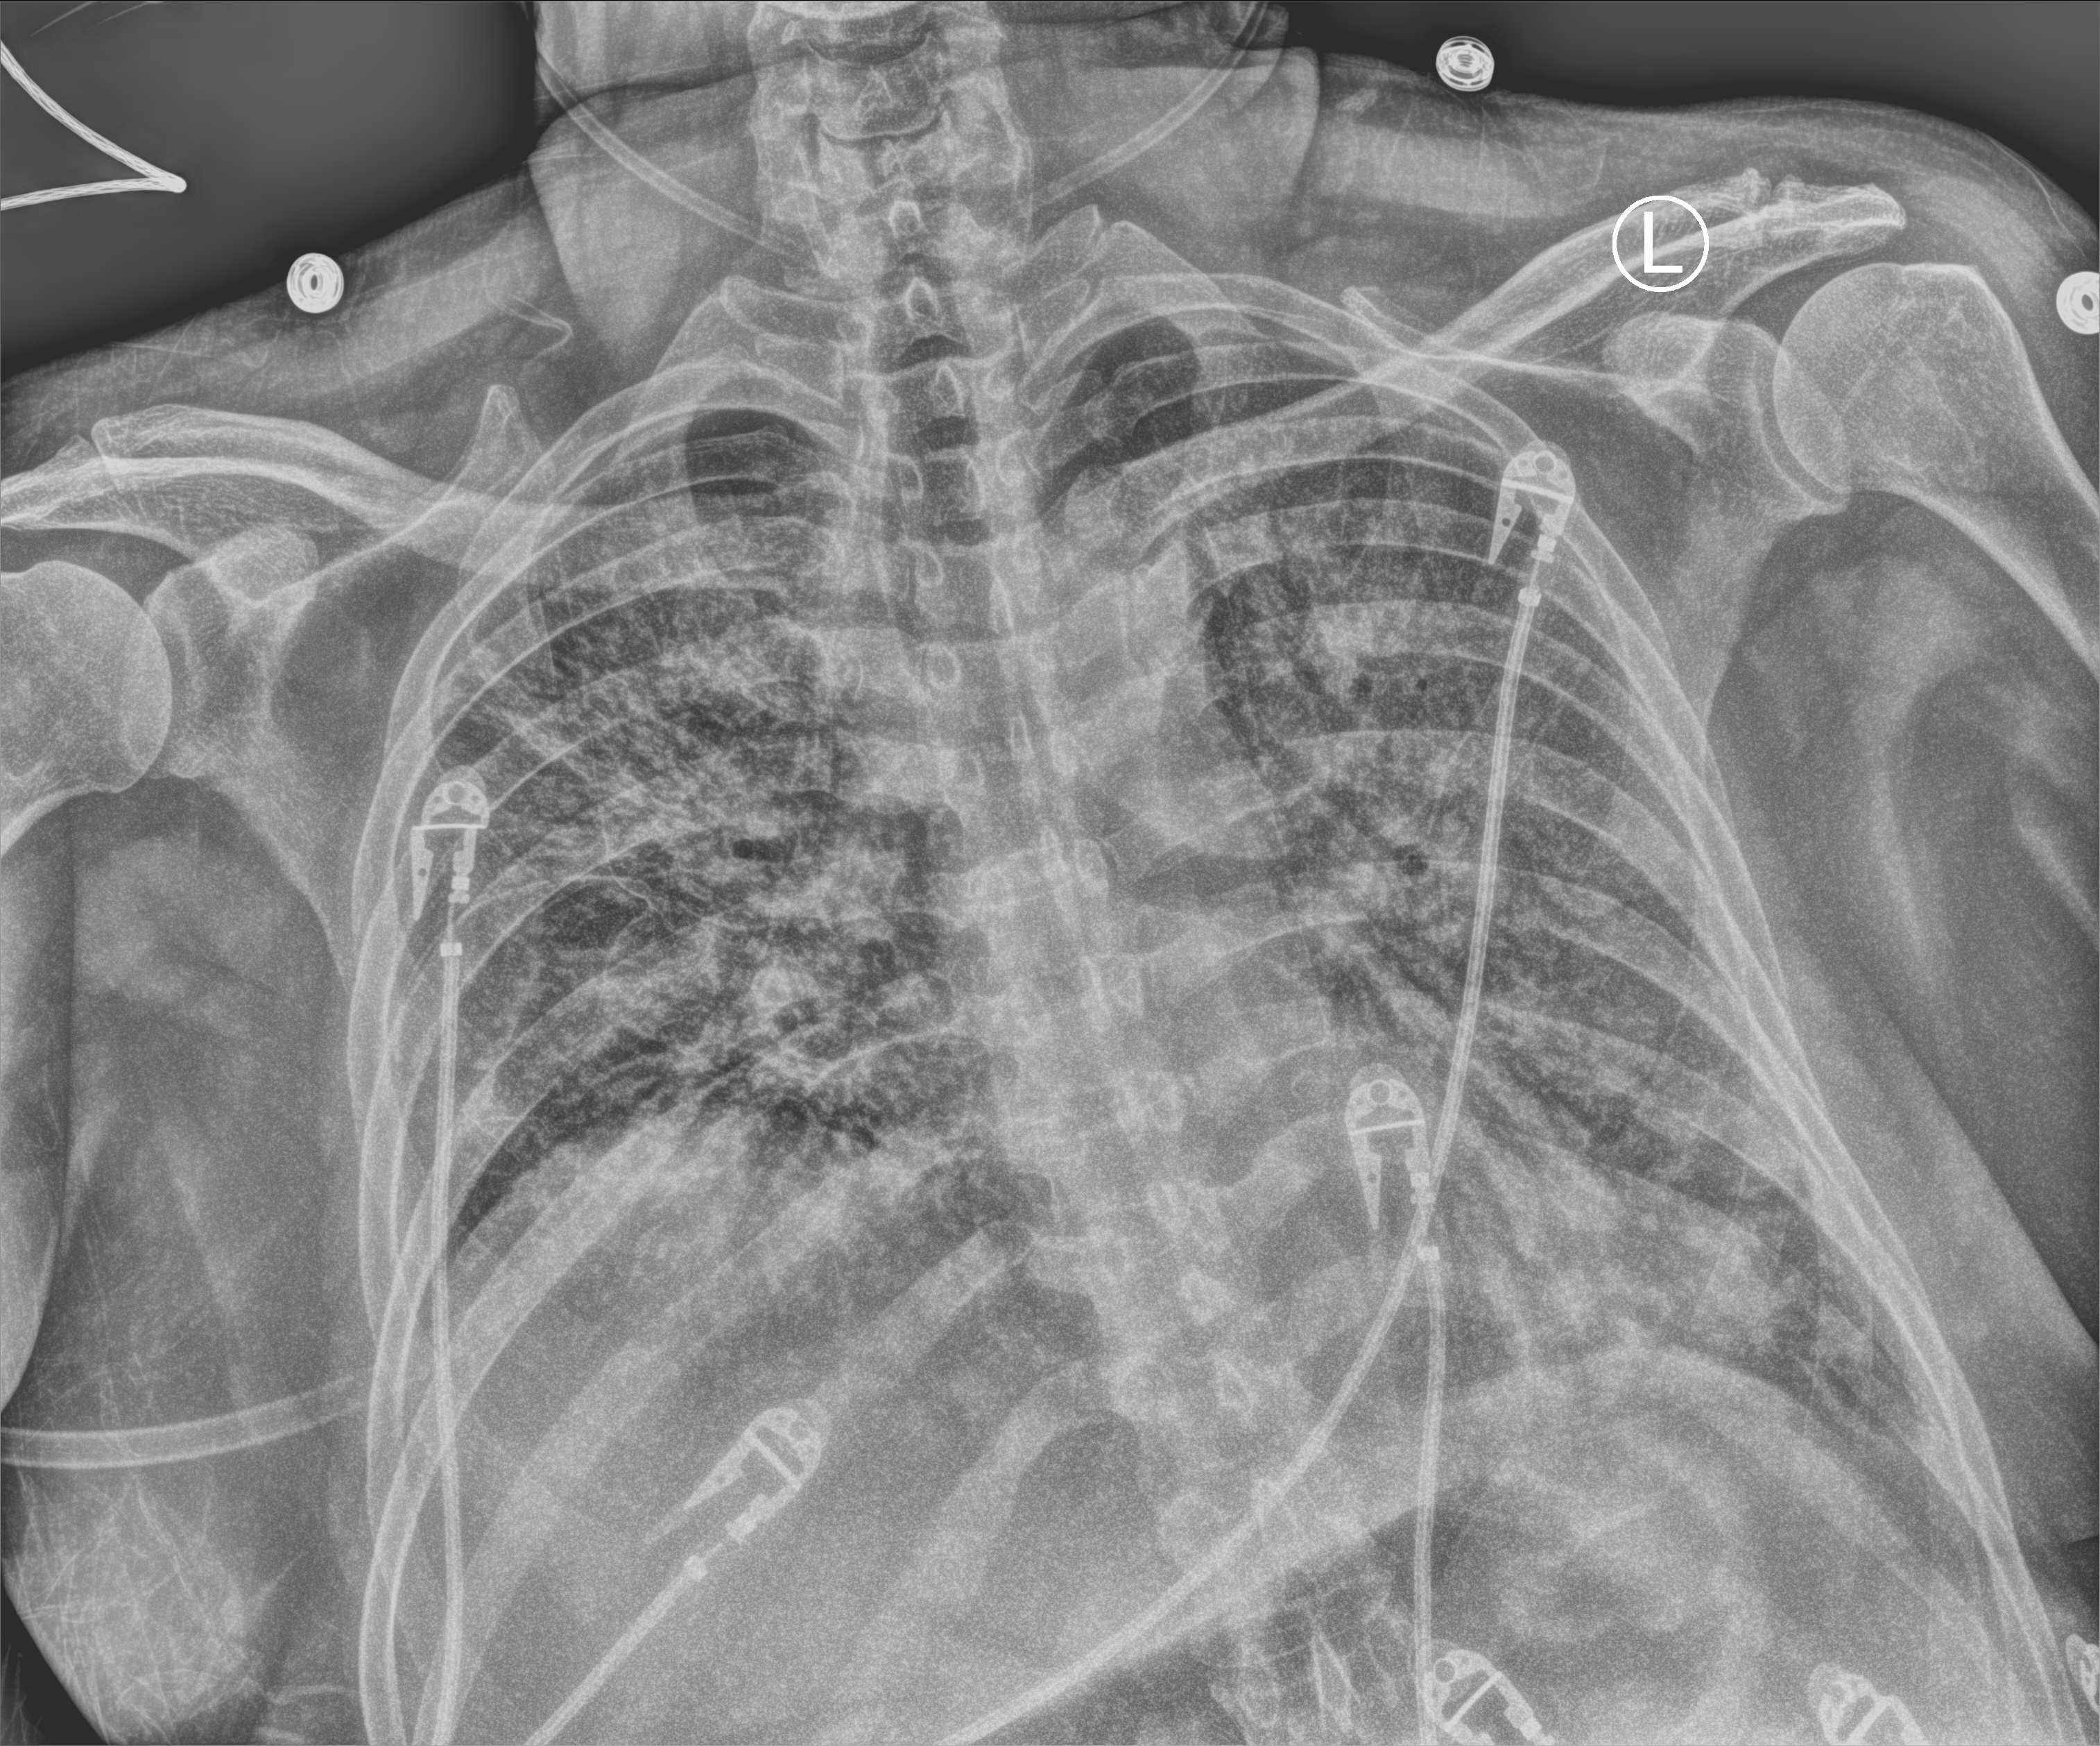
Chest X-ray (portable); anteroposterior (AP) projection. Male patient hospitalised with COVID-19, age 18–59 years.
Admission-level facts for this patient (not findings on this image; timing relative to this image not recorded): admitted to intensive care during this hospital stay: yes; mechanically ventilated during this hospital stay: yes.